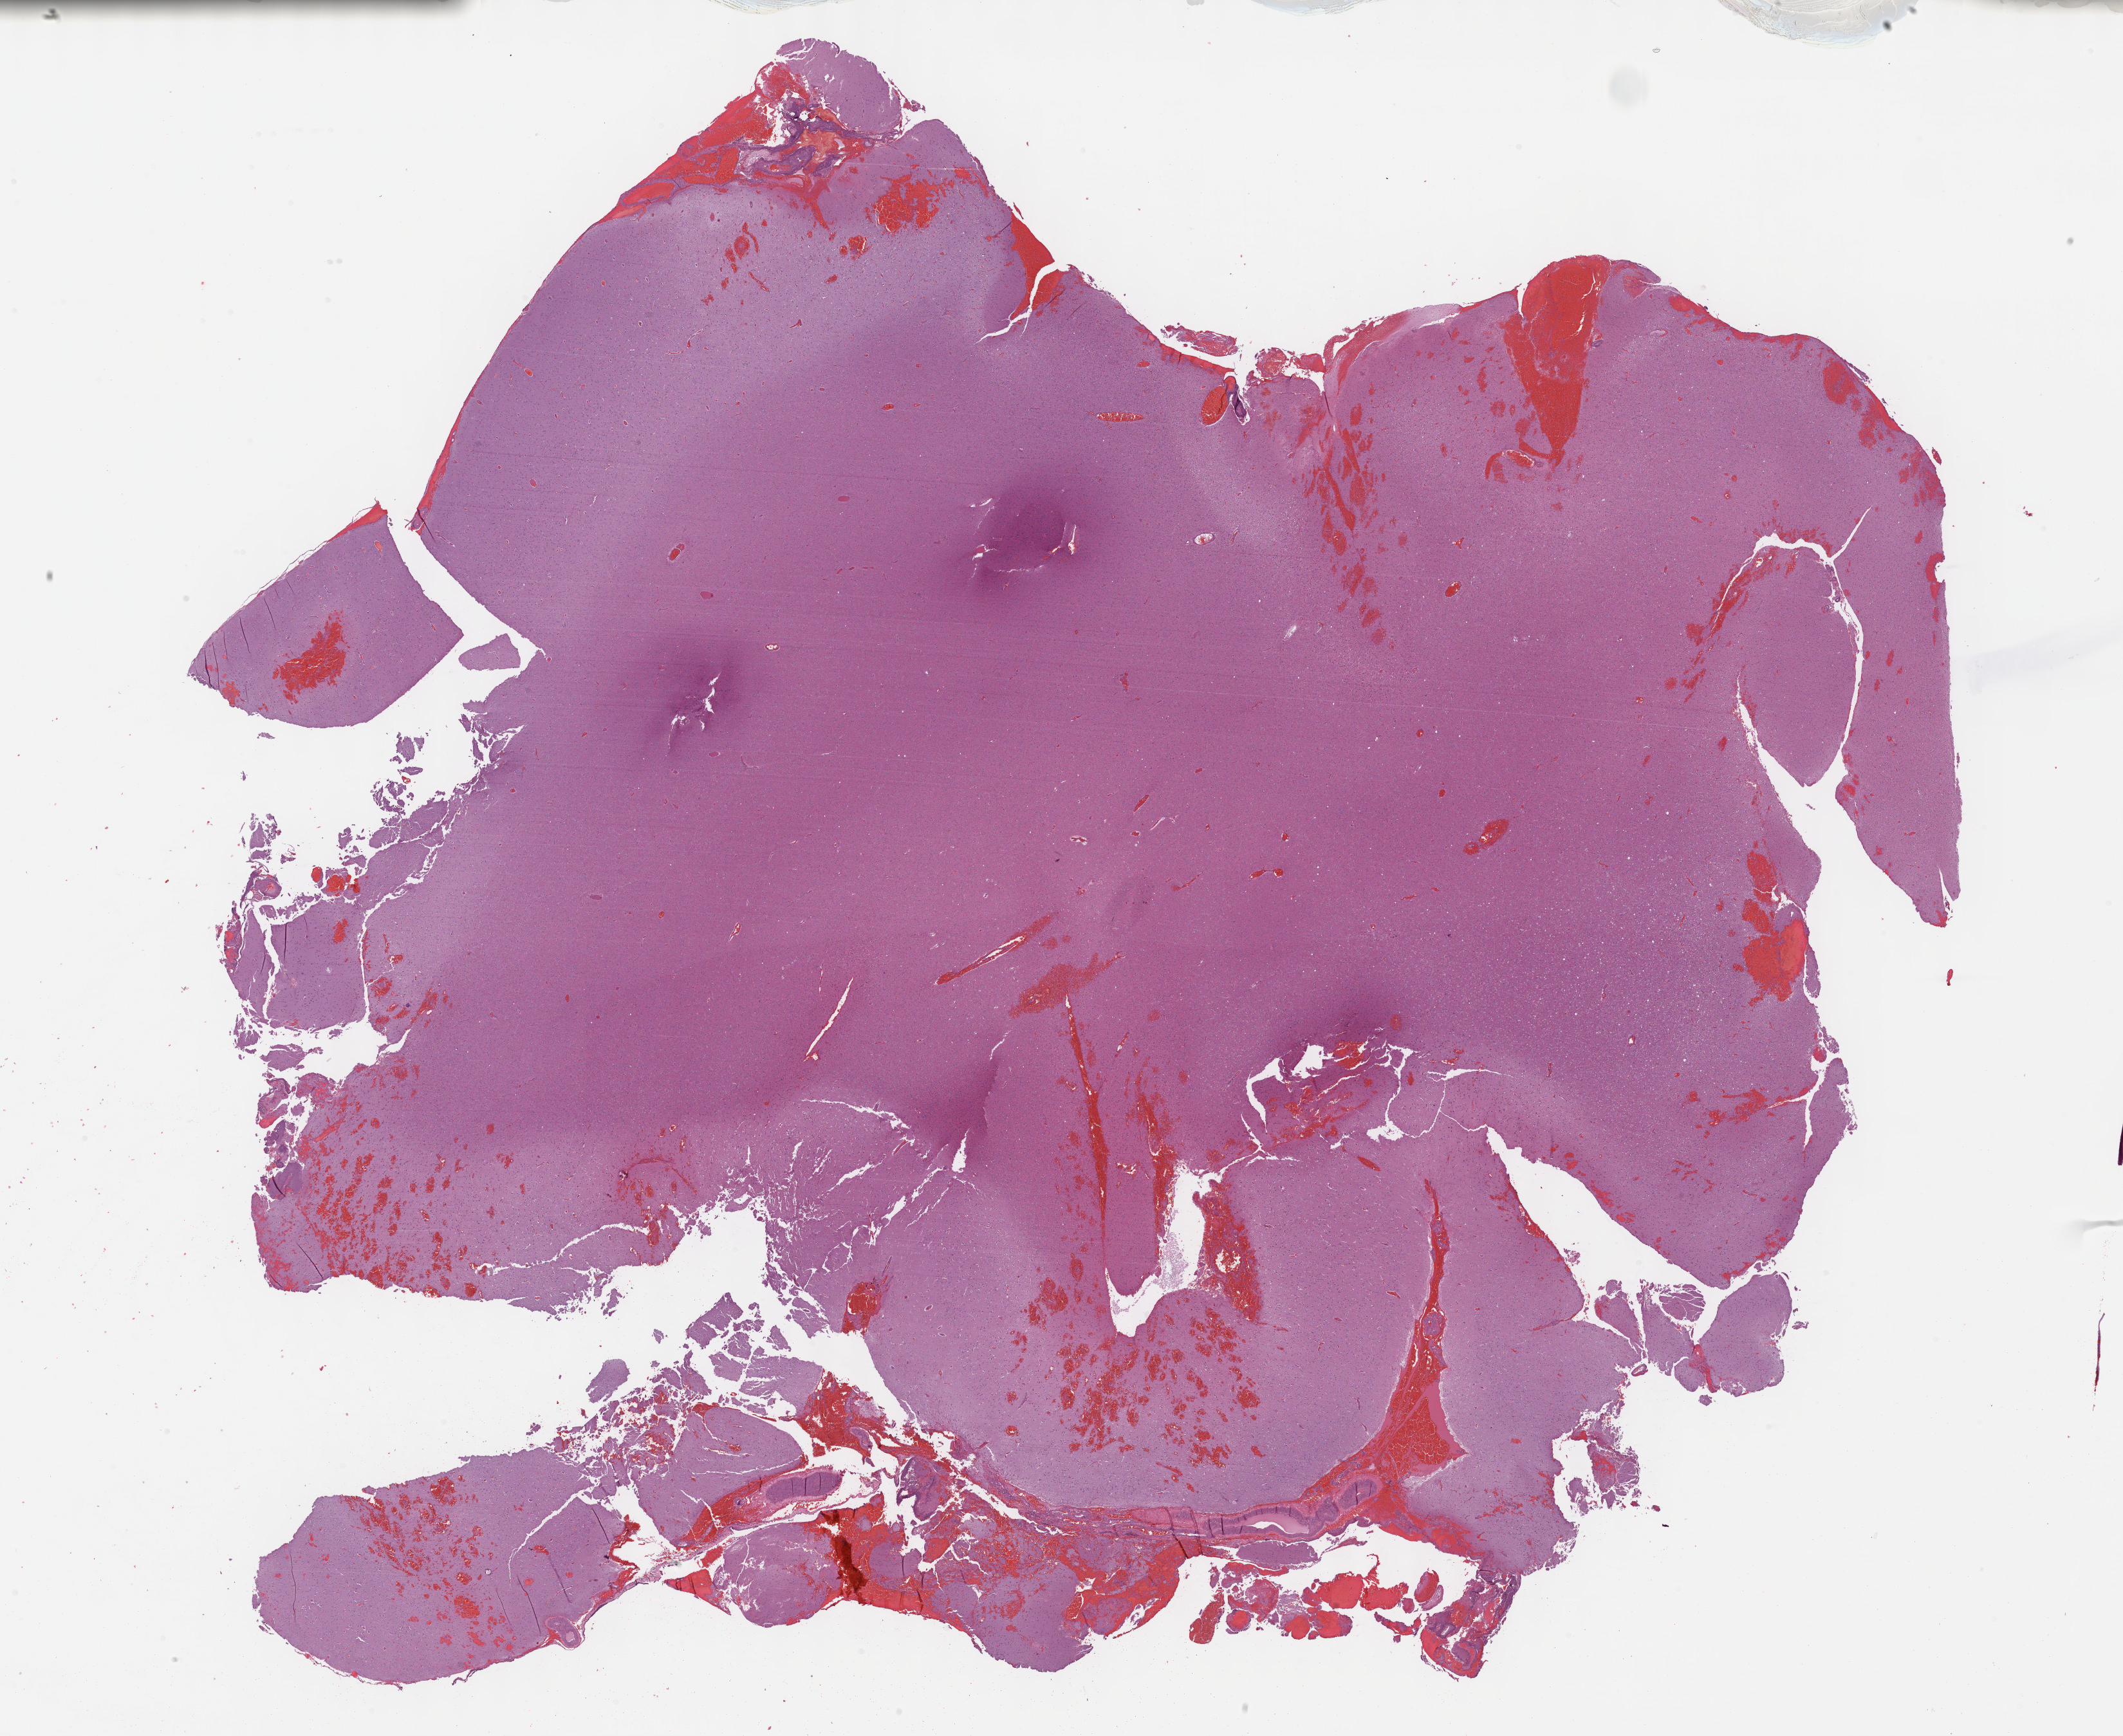
Whole-slide histology image, H&E-stained — a low-resolution overview of the entire scanned area, about 26.7 x 21.8 mm (slide scanned at 40x). FFPE section. Sample: primary tumour, brain. Male, age 61 years at initial diagnosis. Histologic grade: G2 (moderately differentiated).
Pathologic diagnosis: Mixed glioma (cerebrum).